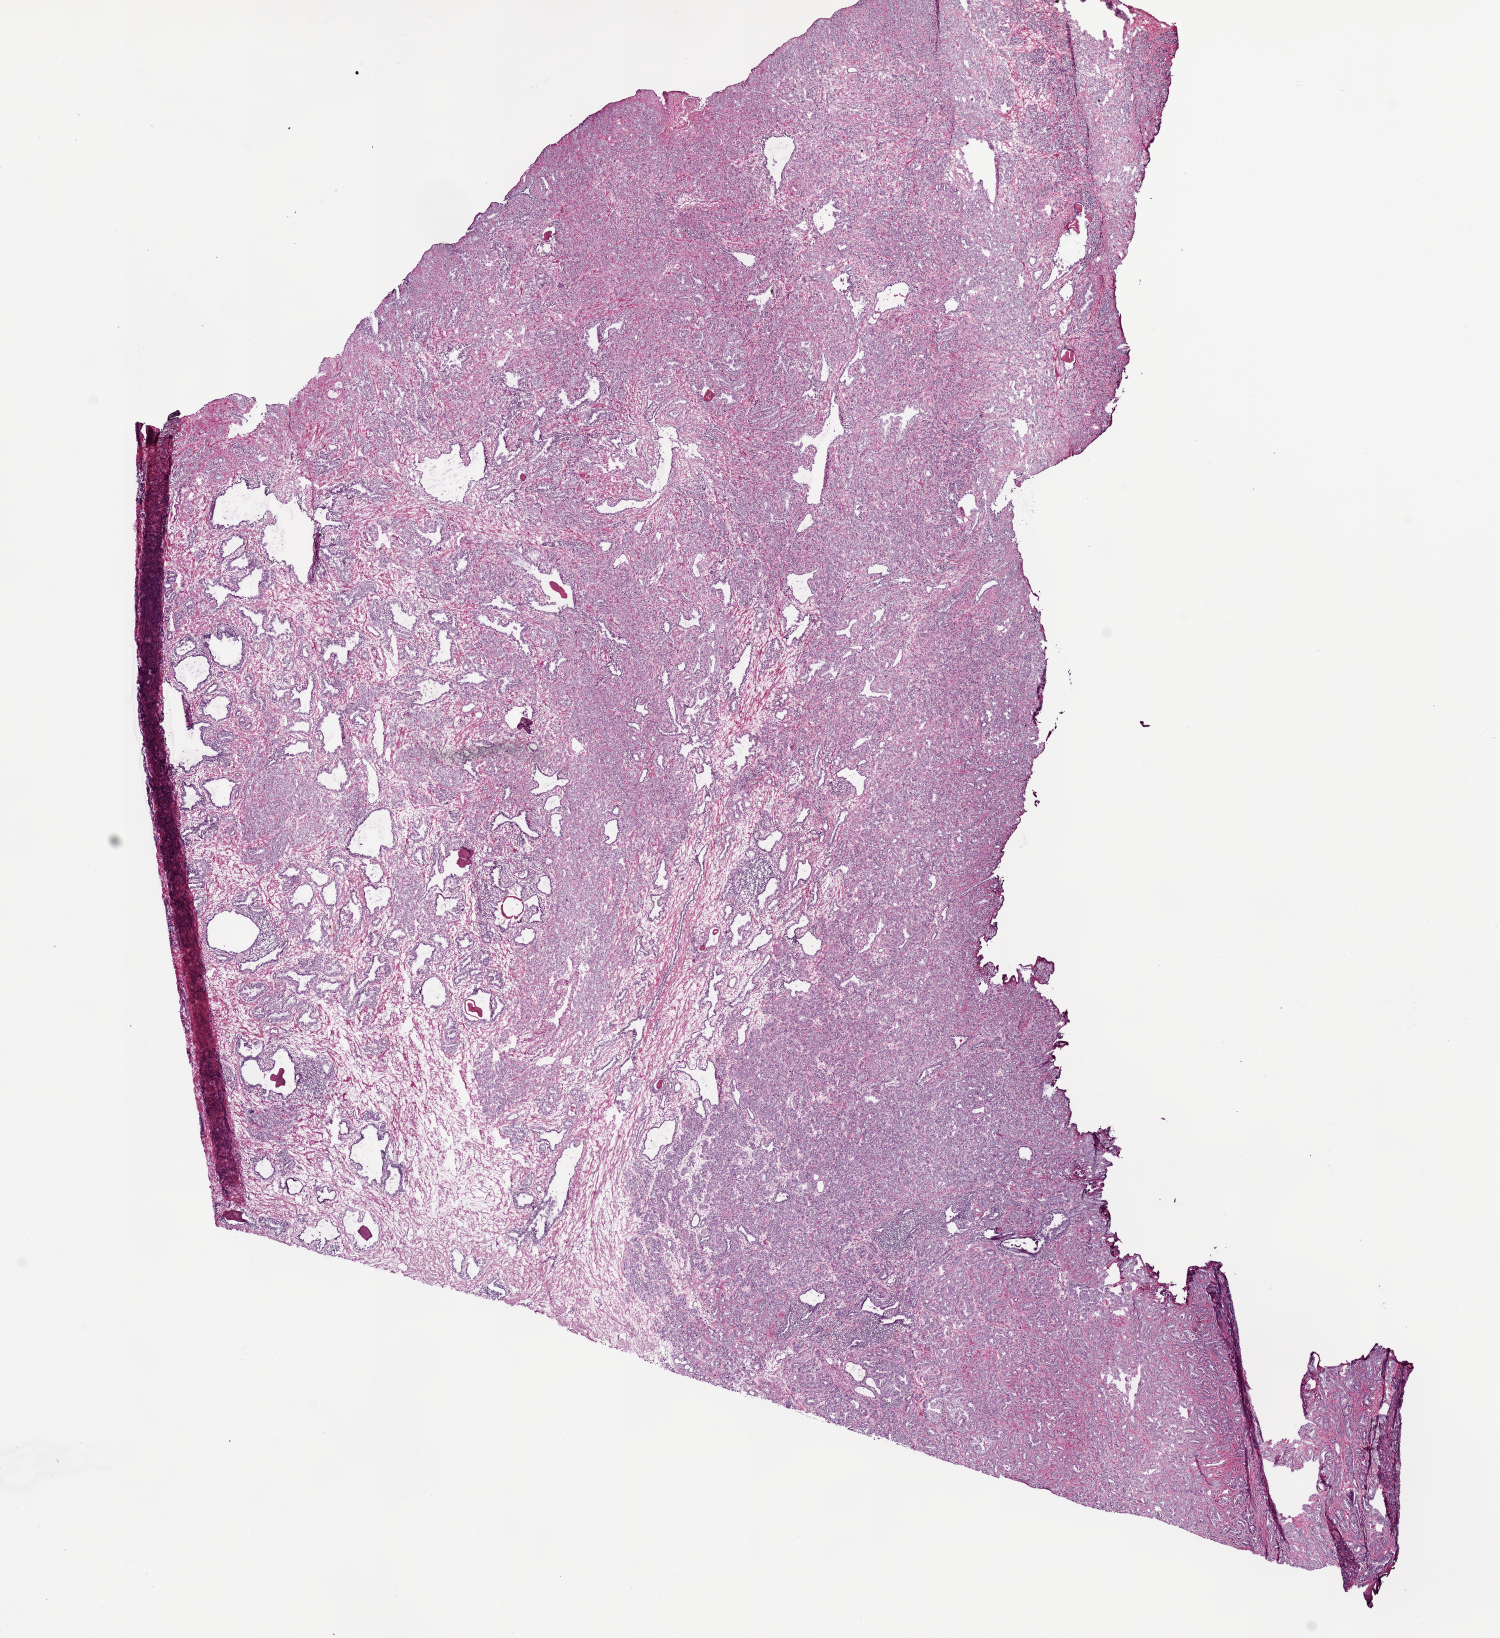
Whole-slide histology image, H&E-stained — shown as a low-resolution overview of the whole scanned area (about 12.0 x 13.1 mm, slide scanned at 20x). Frozen section from the top of the tissue portion. Prostate, primary tumour sample. Patient: male, age at initial diagnosis 50 years. Pathologist review of this section (percent, as recorded): tumour cells 75%, tumour nuclei 80%.
Diagnosis: Acinar cell carcinoma (prostate gland).